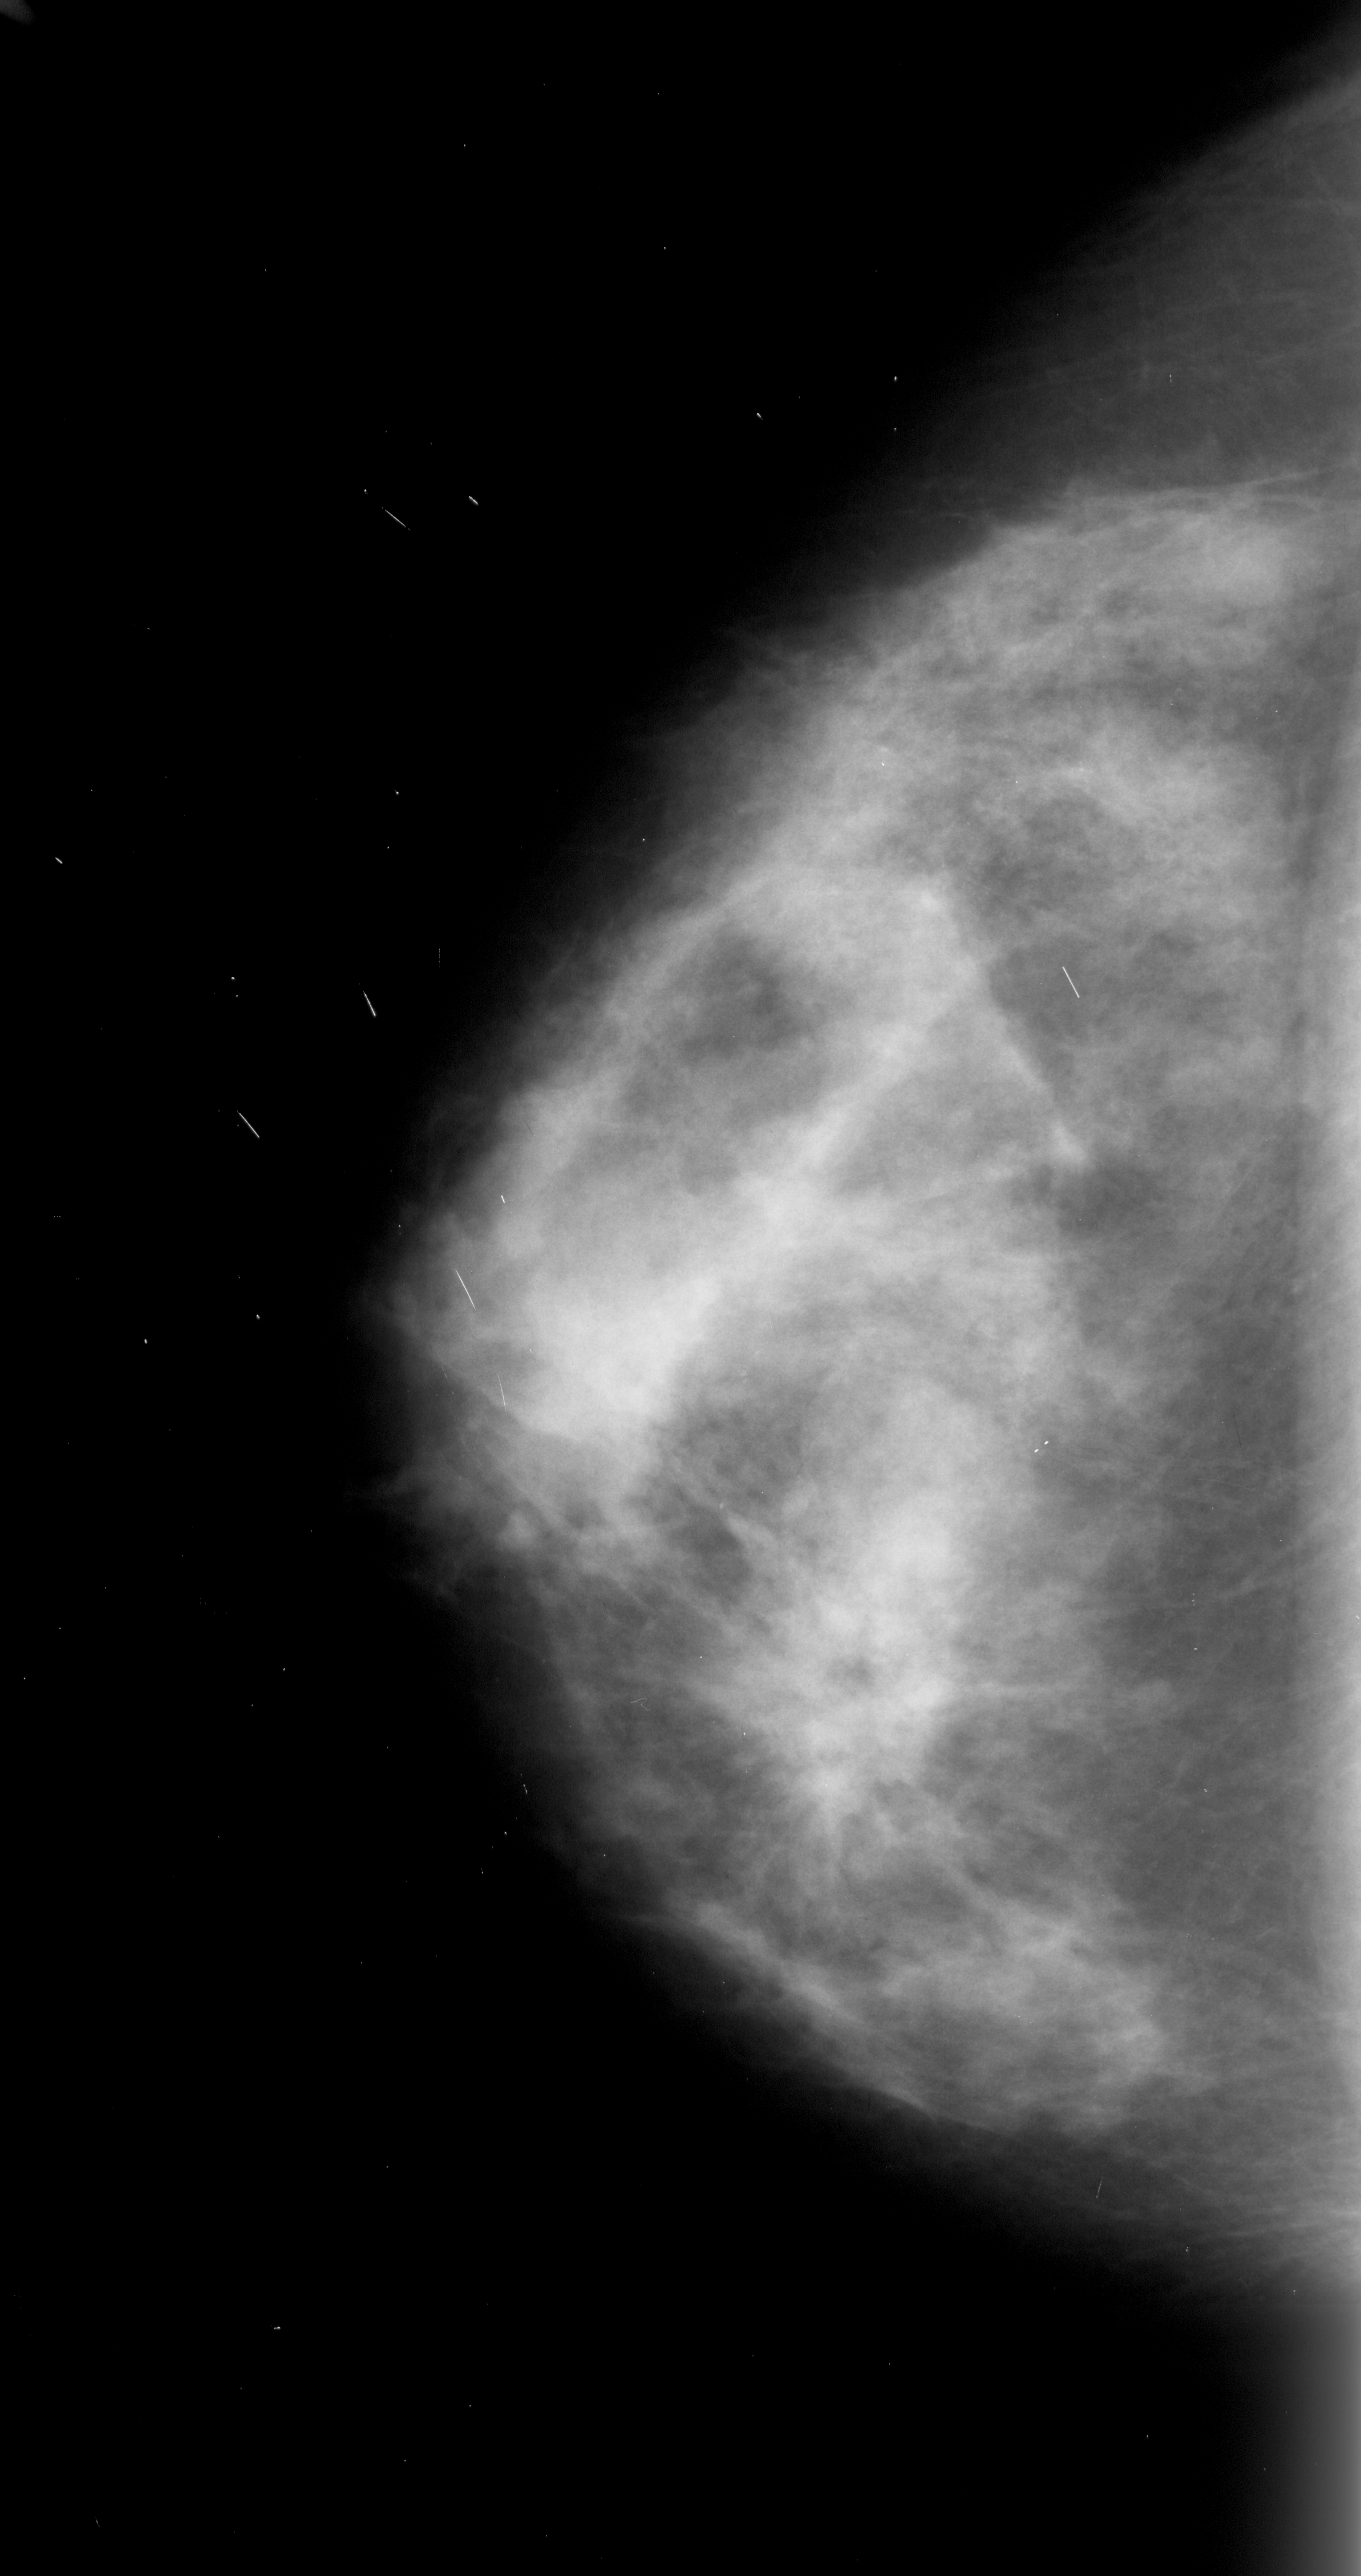
Mammogram (digitized film); left breast; CC view.
Marked findings (only marked abnormalities are described; nothing is implied about the rest of the image): mass, shape irregular, margins spiculated; BI-RADS assessment category 5; subtlety rating 5 on a 1 (subtle) to 5 (obvious) scale; pathology (as recorded): malignant.